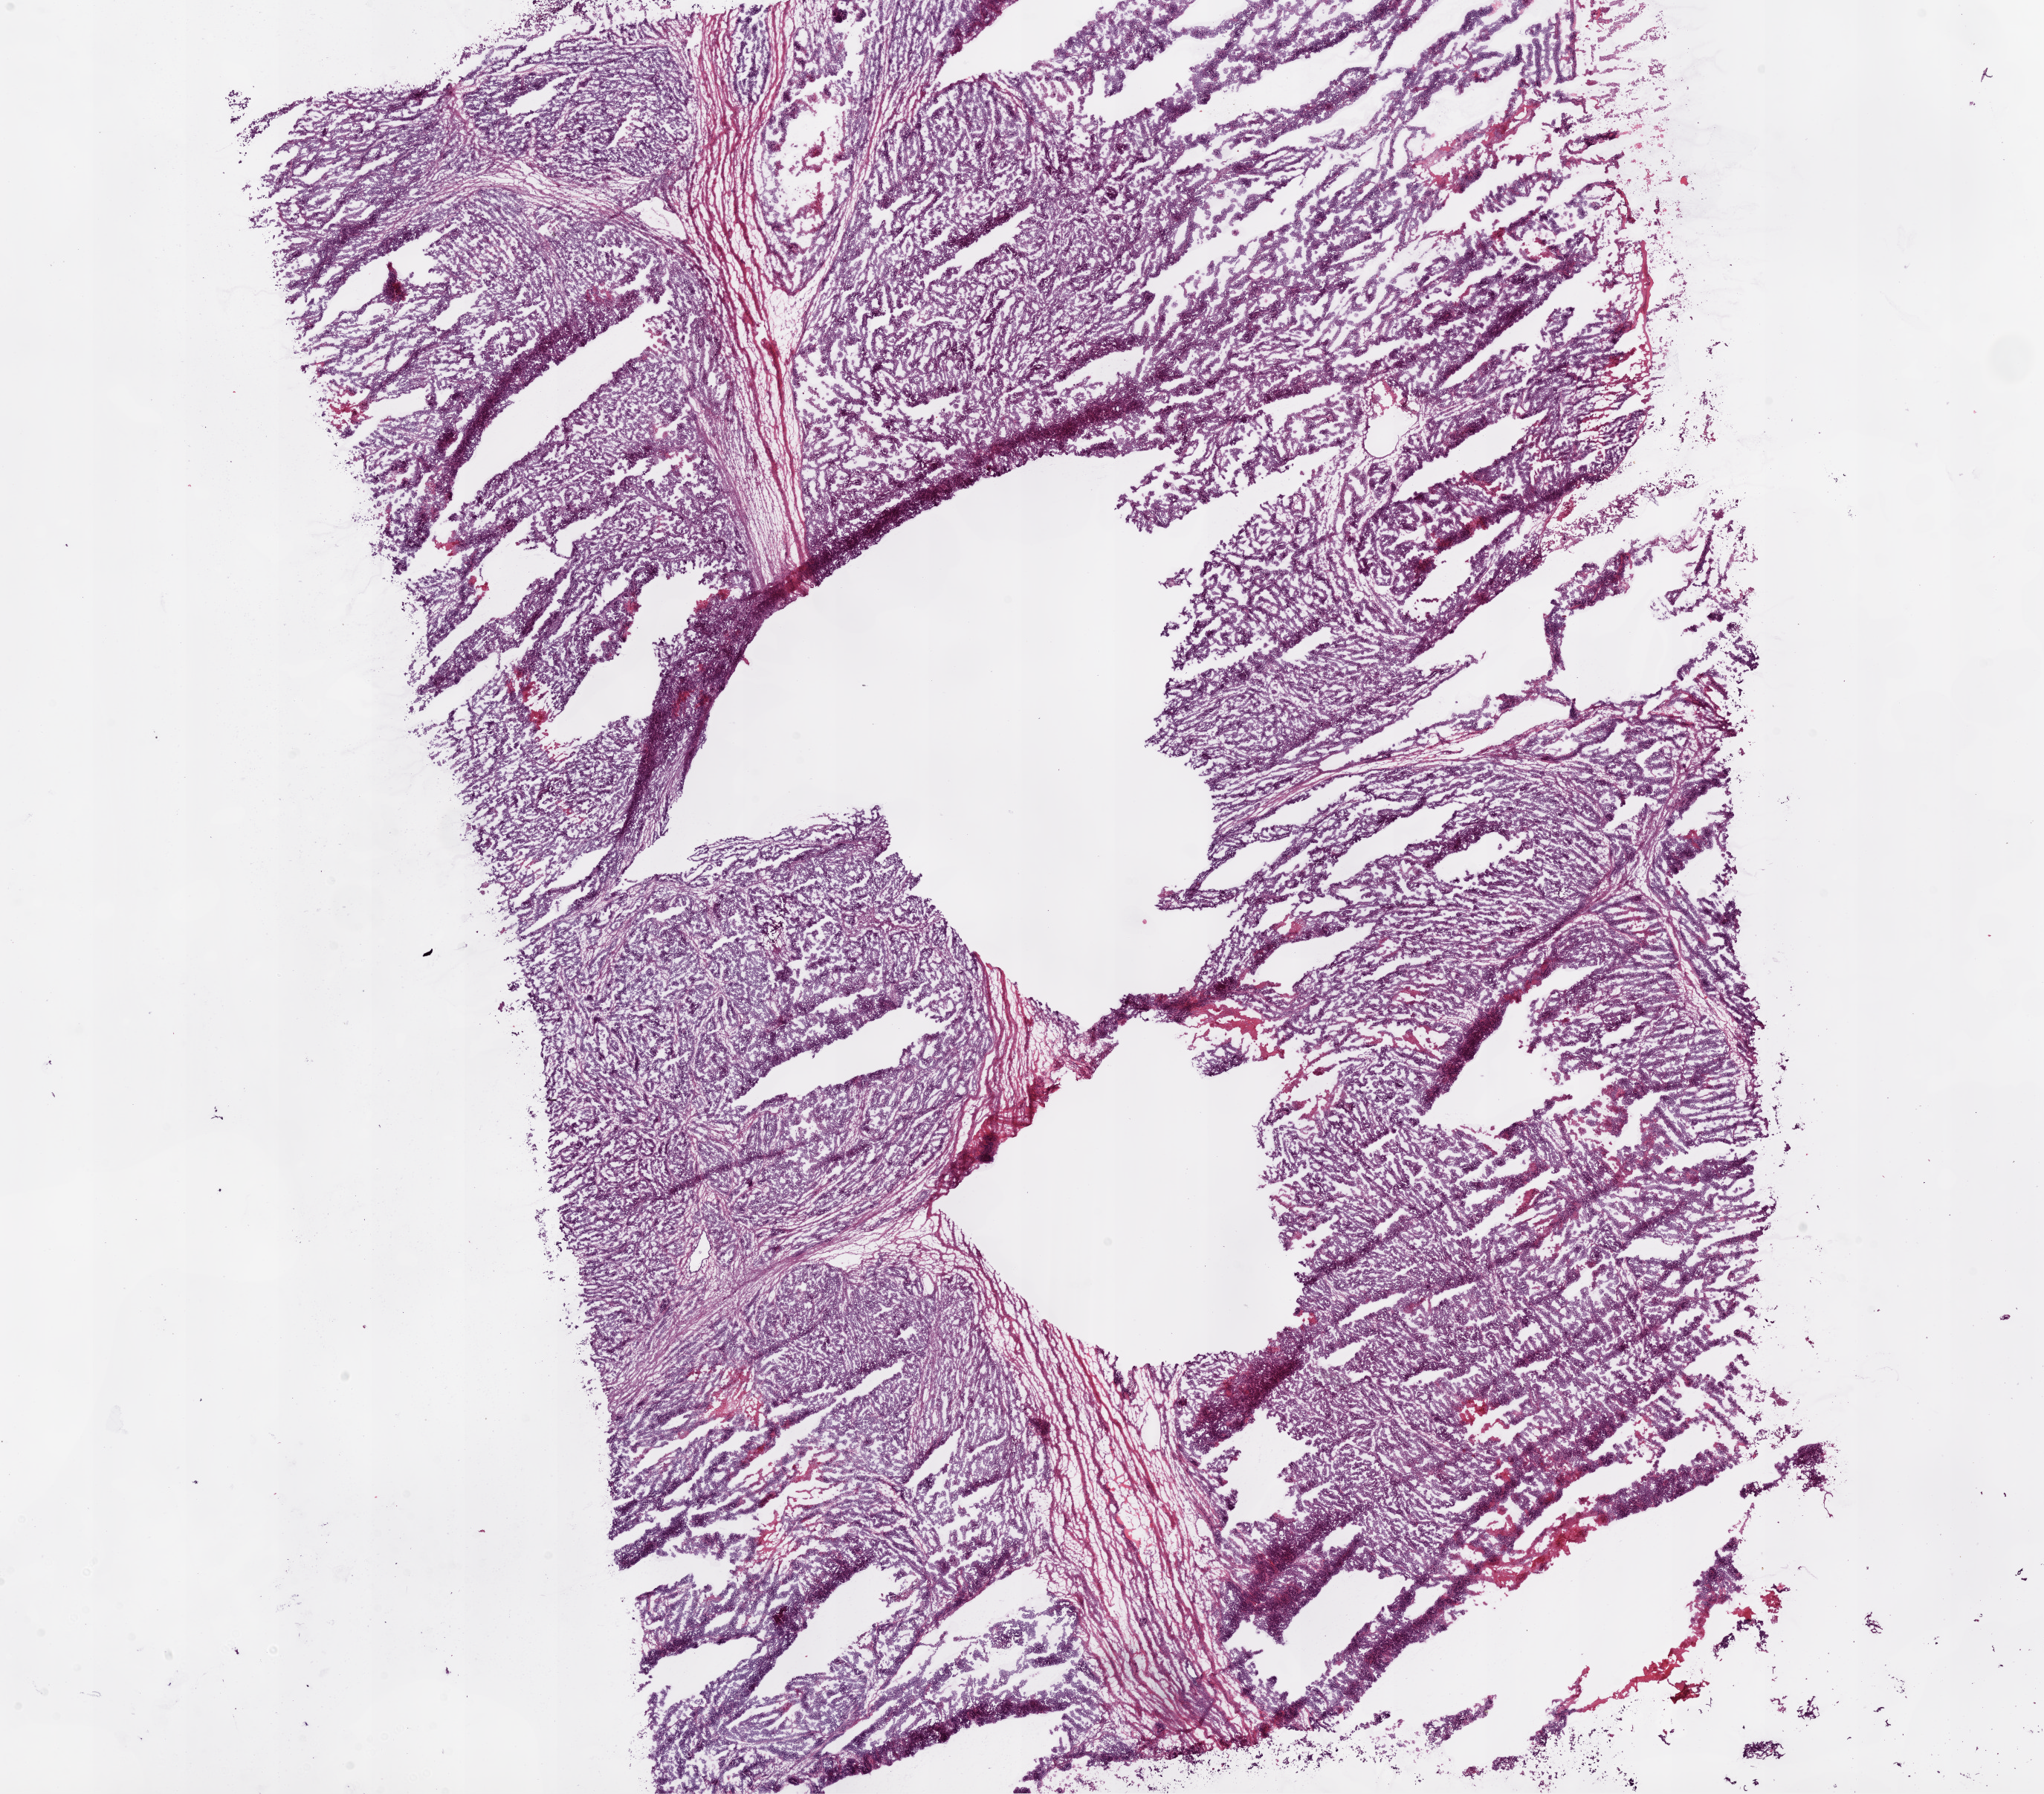
Hematoxylin and eosin (H&E) stained whole-slide image, shown as a low-resolution overview of the whole scanned area (about 22.1 x 19.4 mm). Frozen section from the bottom of the tissue portion. Sample: primary tumour, ovary. Patient: female, age at initial diagnosis 58 years. Histologic grade: G3 (poorly differentiated). Composition of this section per pathologist review: tumour cells 88%, tumour nuclei 75%, normal cells 0%, stromal cells 10%, necrosis 2%. Infiltration values recorded for this section: lymphocyte infiltration 15%, monocyte infiltration 5%, neutrophil infiltration 0%.
- FIGO stage: IIIC
- histologic diagnosis: Serous cystadenocarcinoma, NOS
- laterality: bilateral